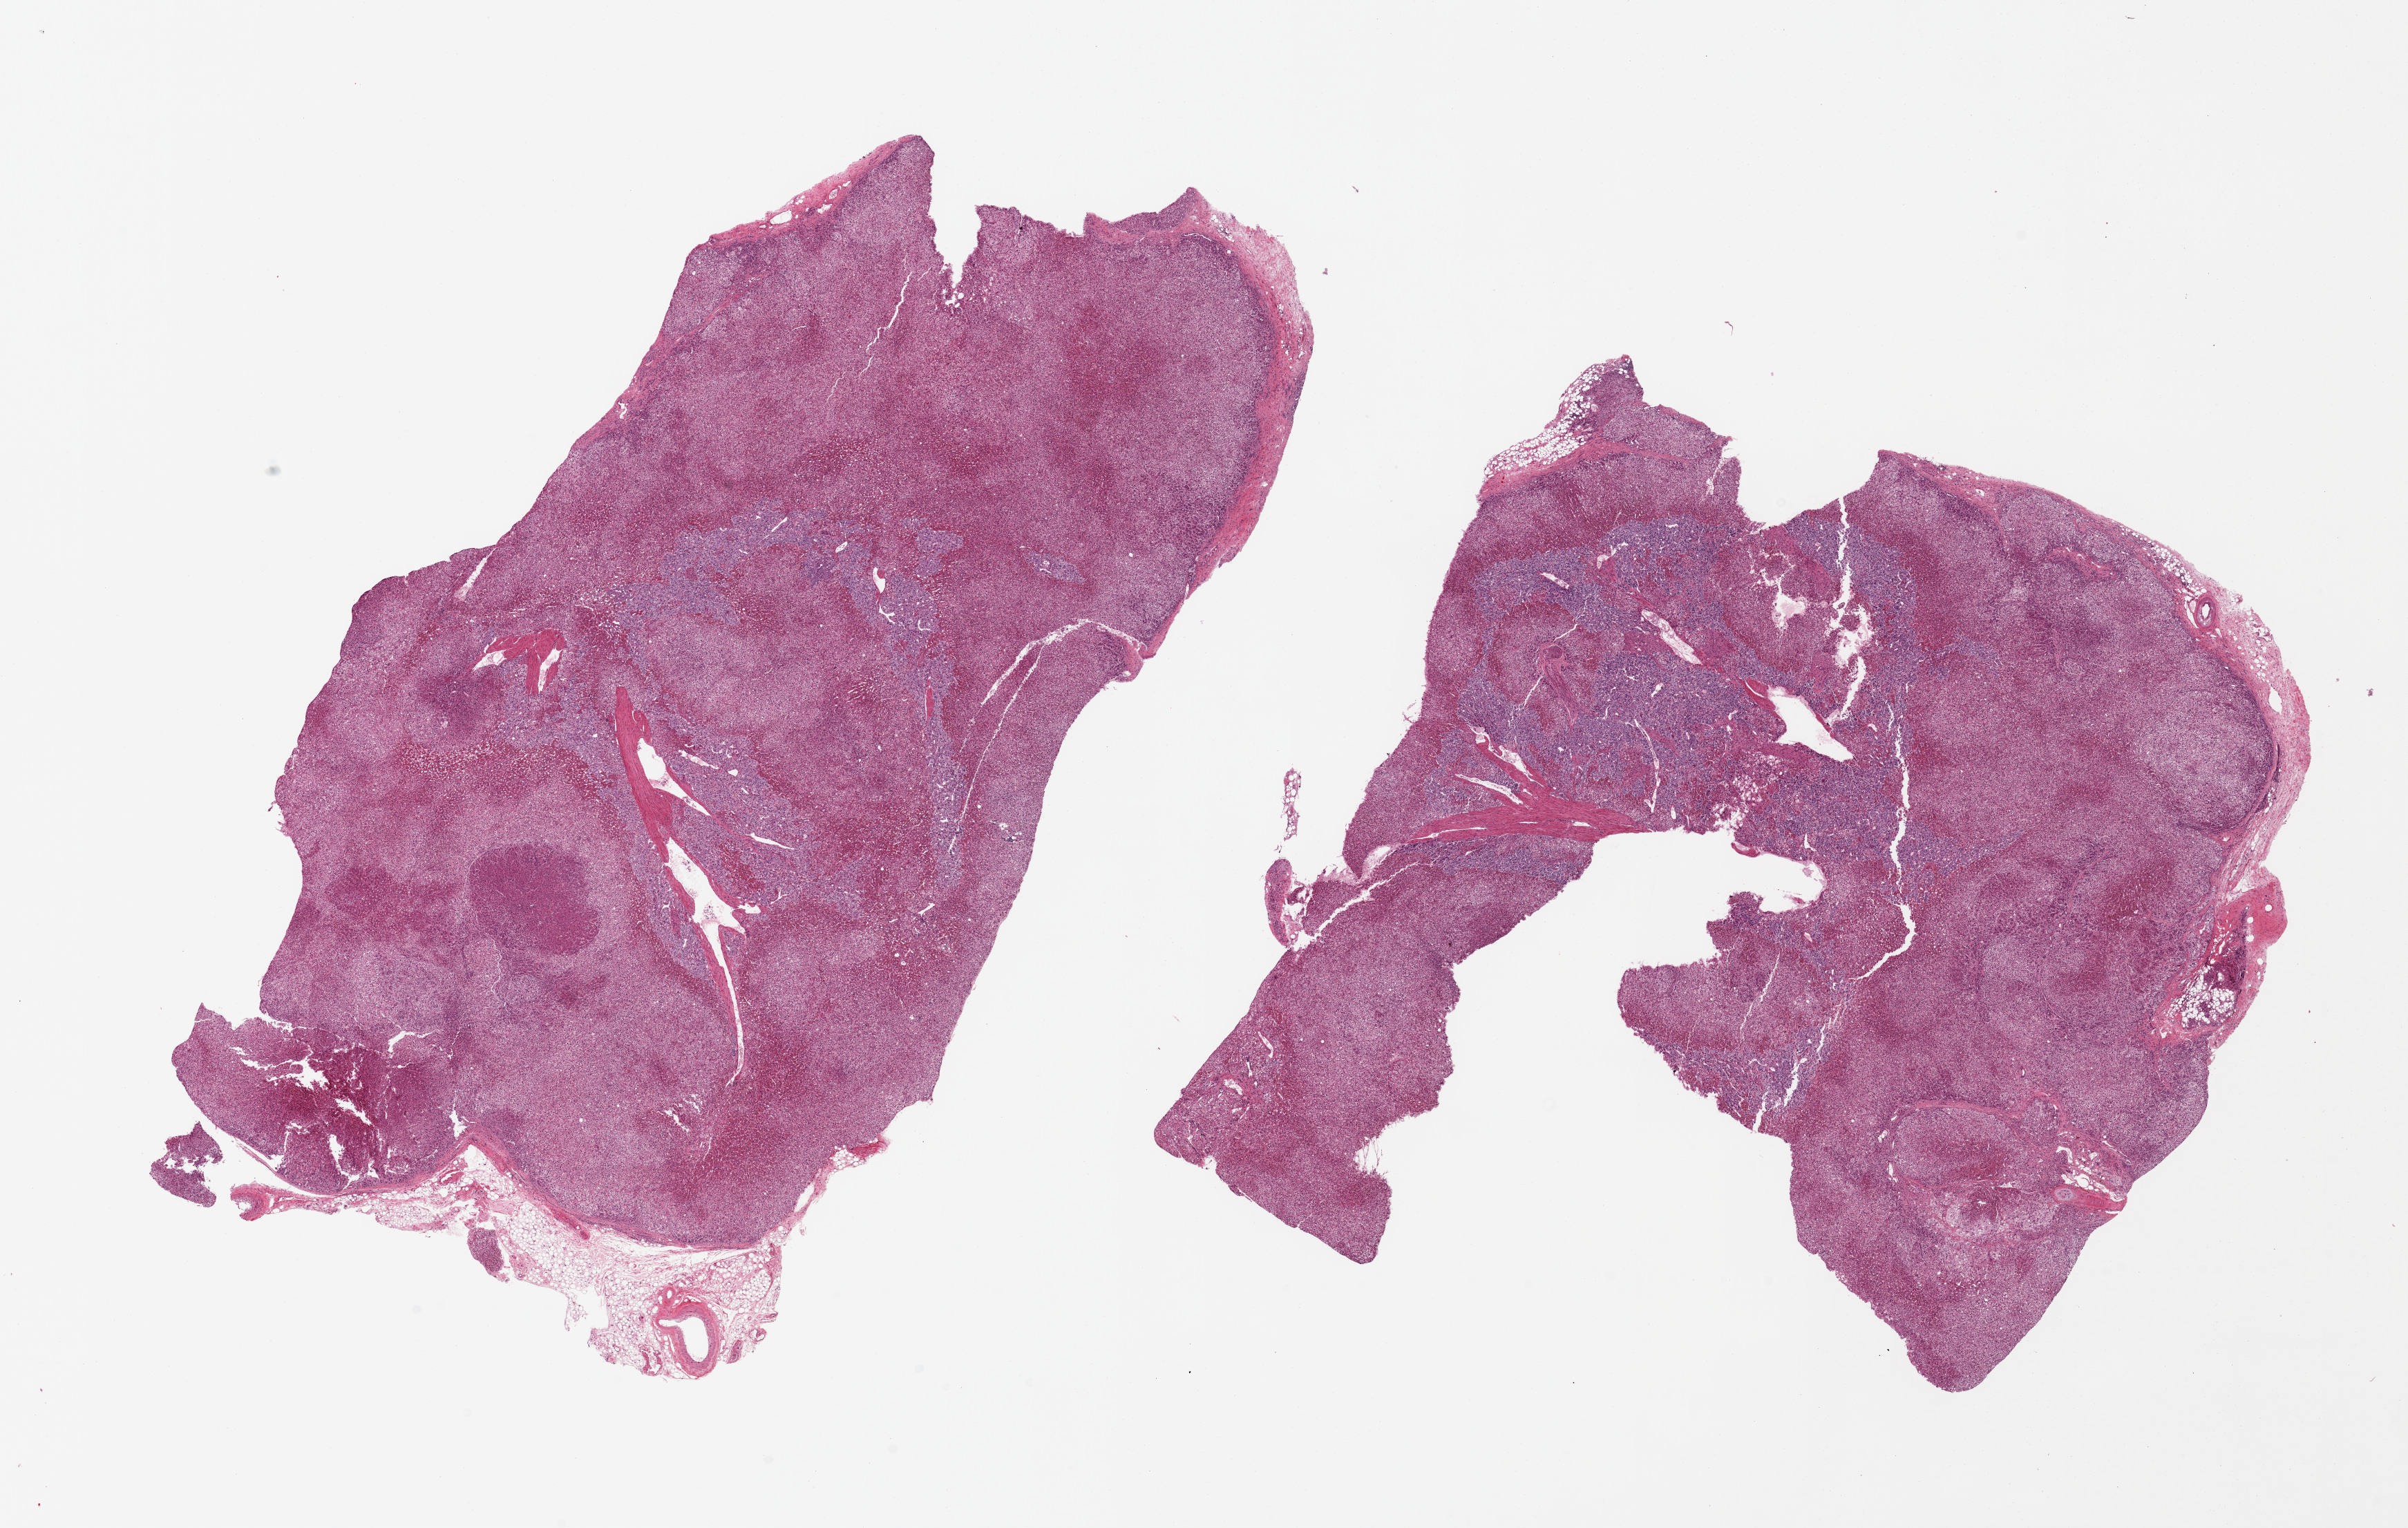
Whole-slide image, H&E stain — a low-resolution overview of the entire scanned area, about 27.6 x 17.5 mm (from a 20x scan), PAXgene-fixed, paraffin-embedded tissue, target tissue: adrenal gland, tissue donor sample. Male donor.
Reviewer comment on this tissue sample: 2 pieces. Moderate medullary hyperplasia.